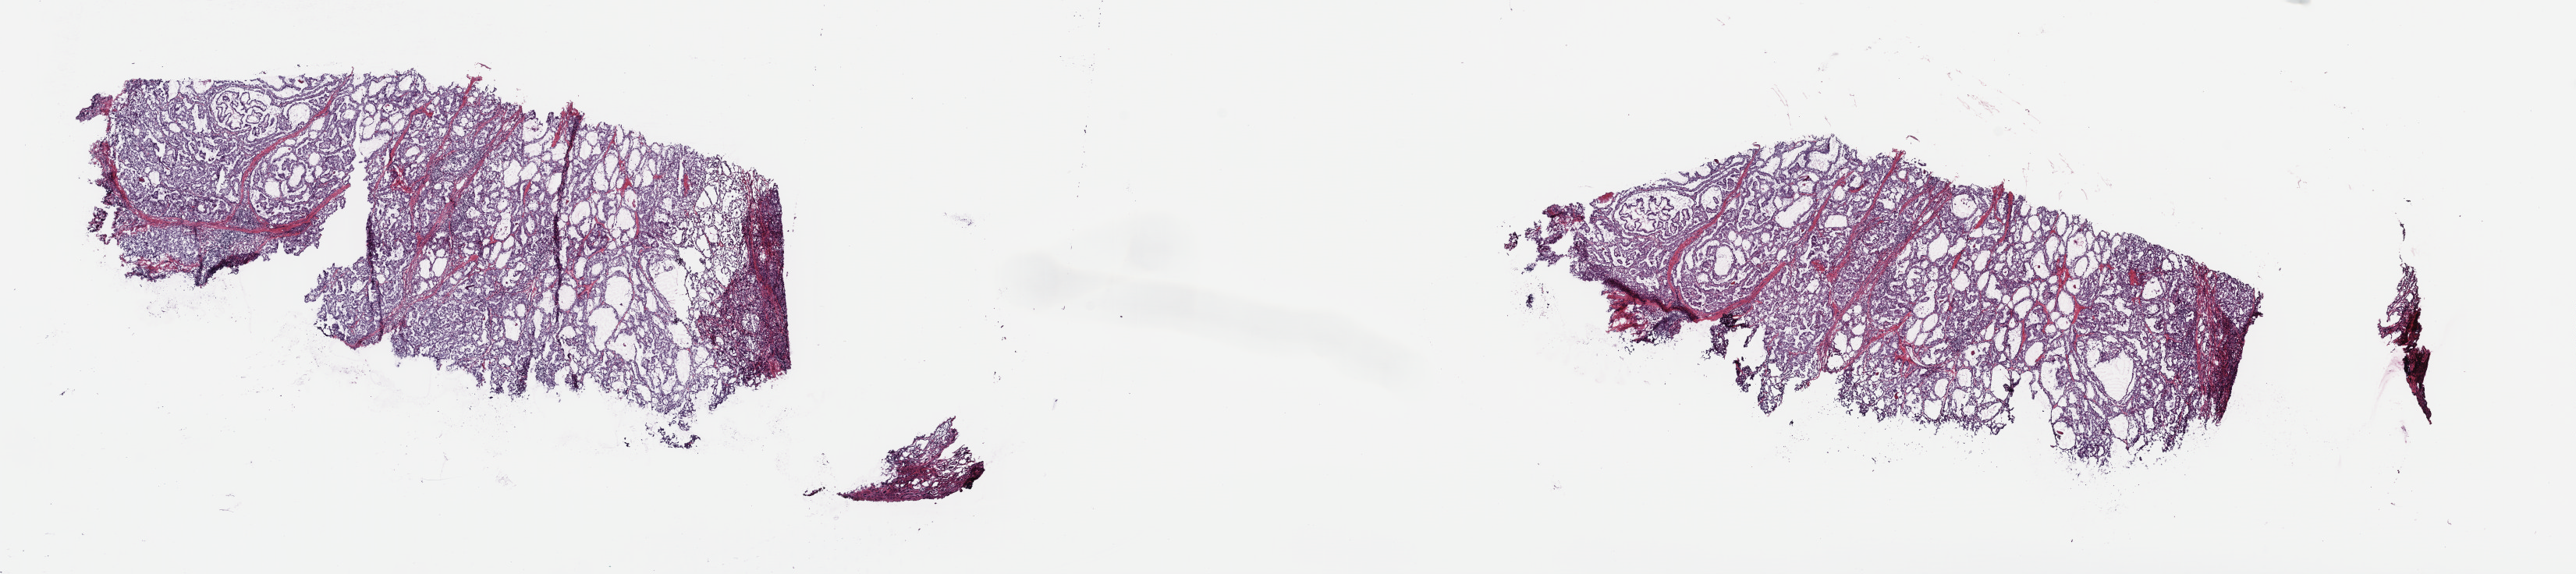
Whole-slide histology image, H&E-stained, shown as a low-resolution overview of the whole scanned area (about 26.0 x 5.8 mm, acquisition: 40x scan). Frozen section from the top of the tissue portion. Thyroid, primary tumour sample. Female patient; age at initial diagnosis 36 years. Pathologist review of this section (percent, as recorded): tumour cells 75%, tumour nuclei 75%, normal cells 2%, stromal cells 23%, necrosis 0%. Infiltration values recorded for this section: lymphocyte infiltration 2%, monocyte infiltration 1%, neutrophil infiltration 0%.
TNM: T2 N0 M0. AJCC pathologic stage: I. Histologic diagnosis: Papillary adenocarcinoma, NOS (thyroid gland).